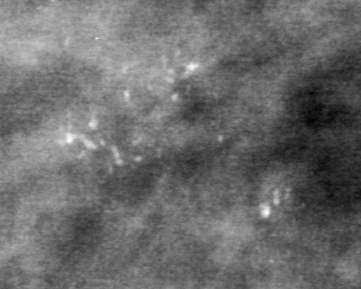
Crop from a digitized film mammogram around one marked abnormality, left breast, MLO view.
Finding: calcifications, morphology pleomorphic, distribution clustered; BI-RADS assessment category 4; subtlety rating 4 on a 1 (subtle) to 5 (obvious) scale; pathology result (as recorded, not read from the image): malignant.